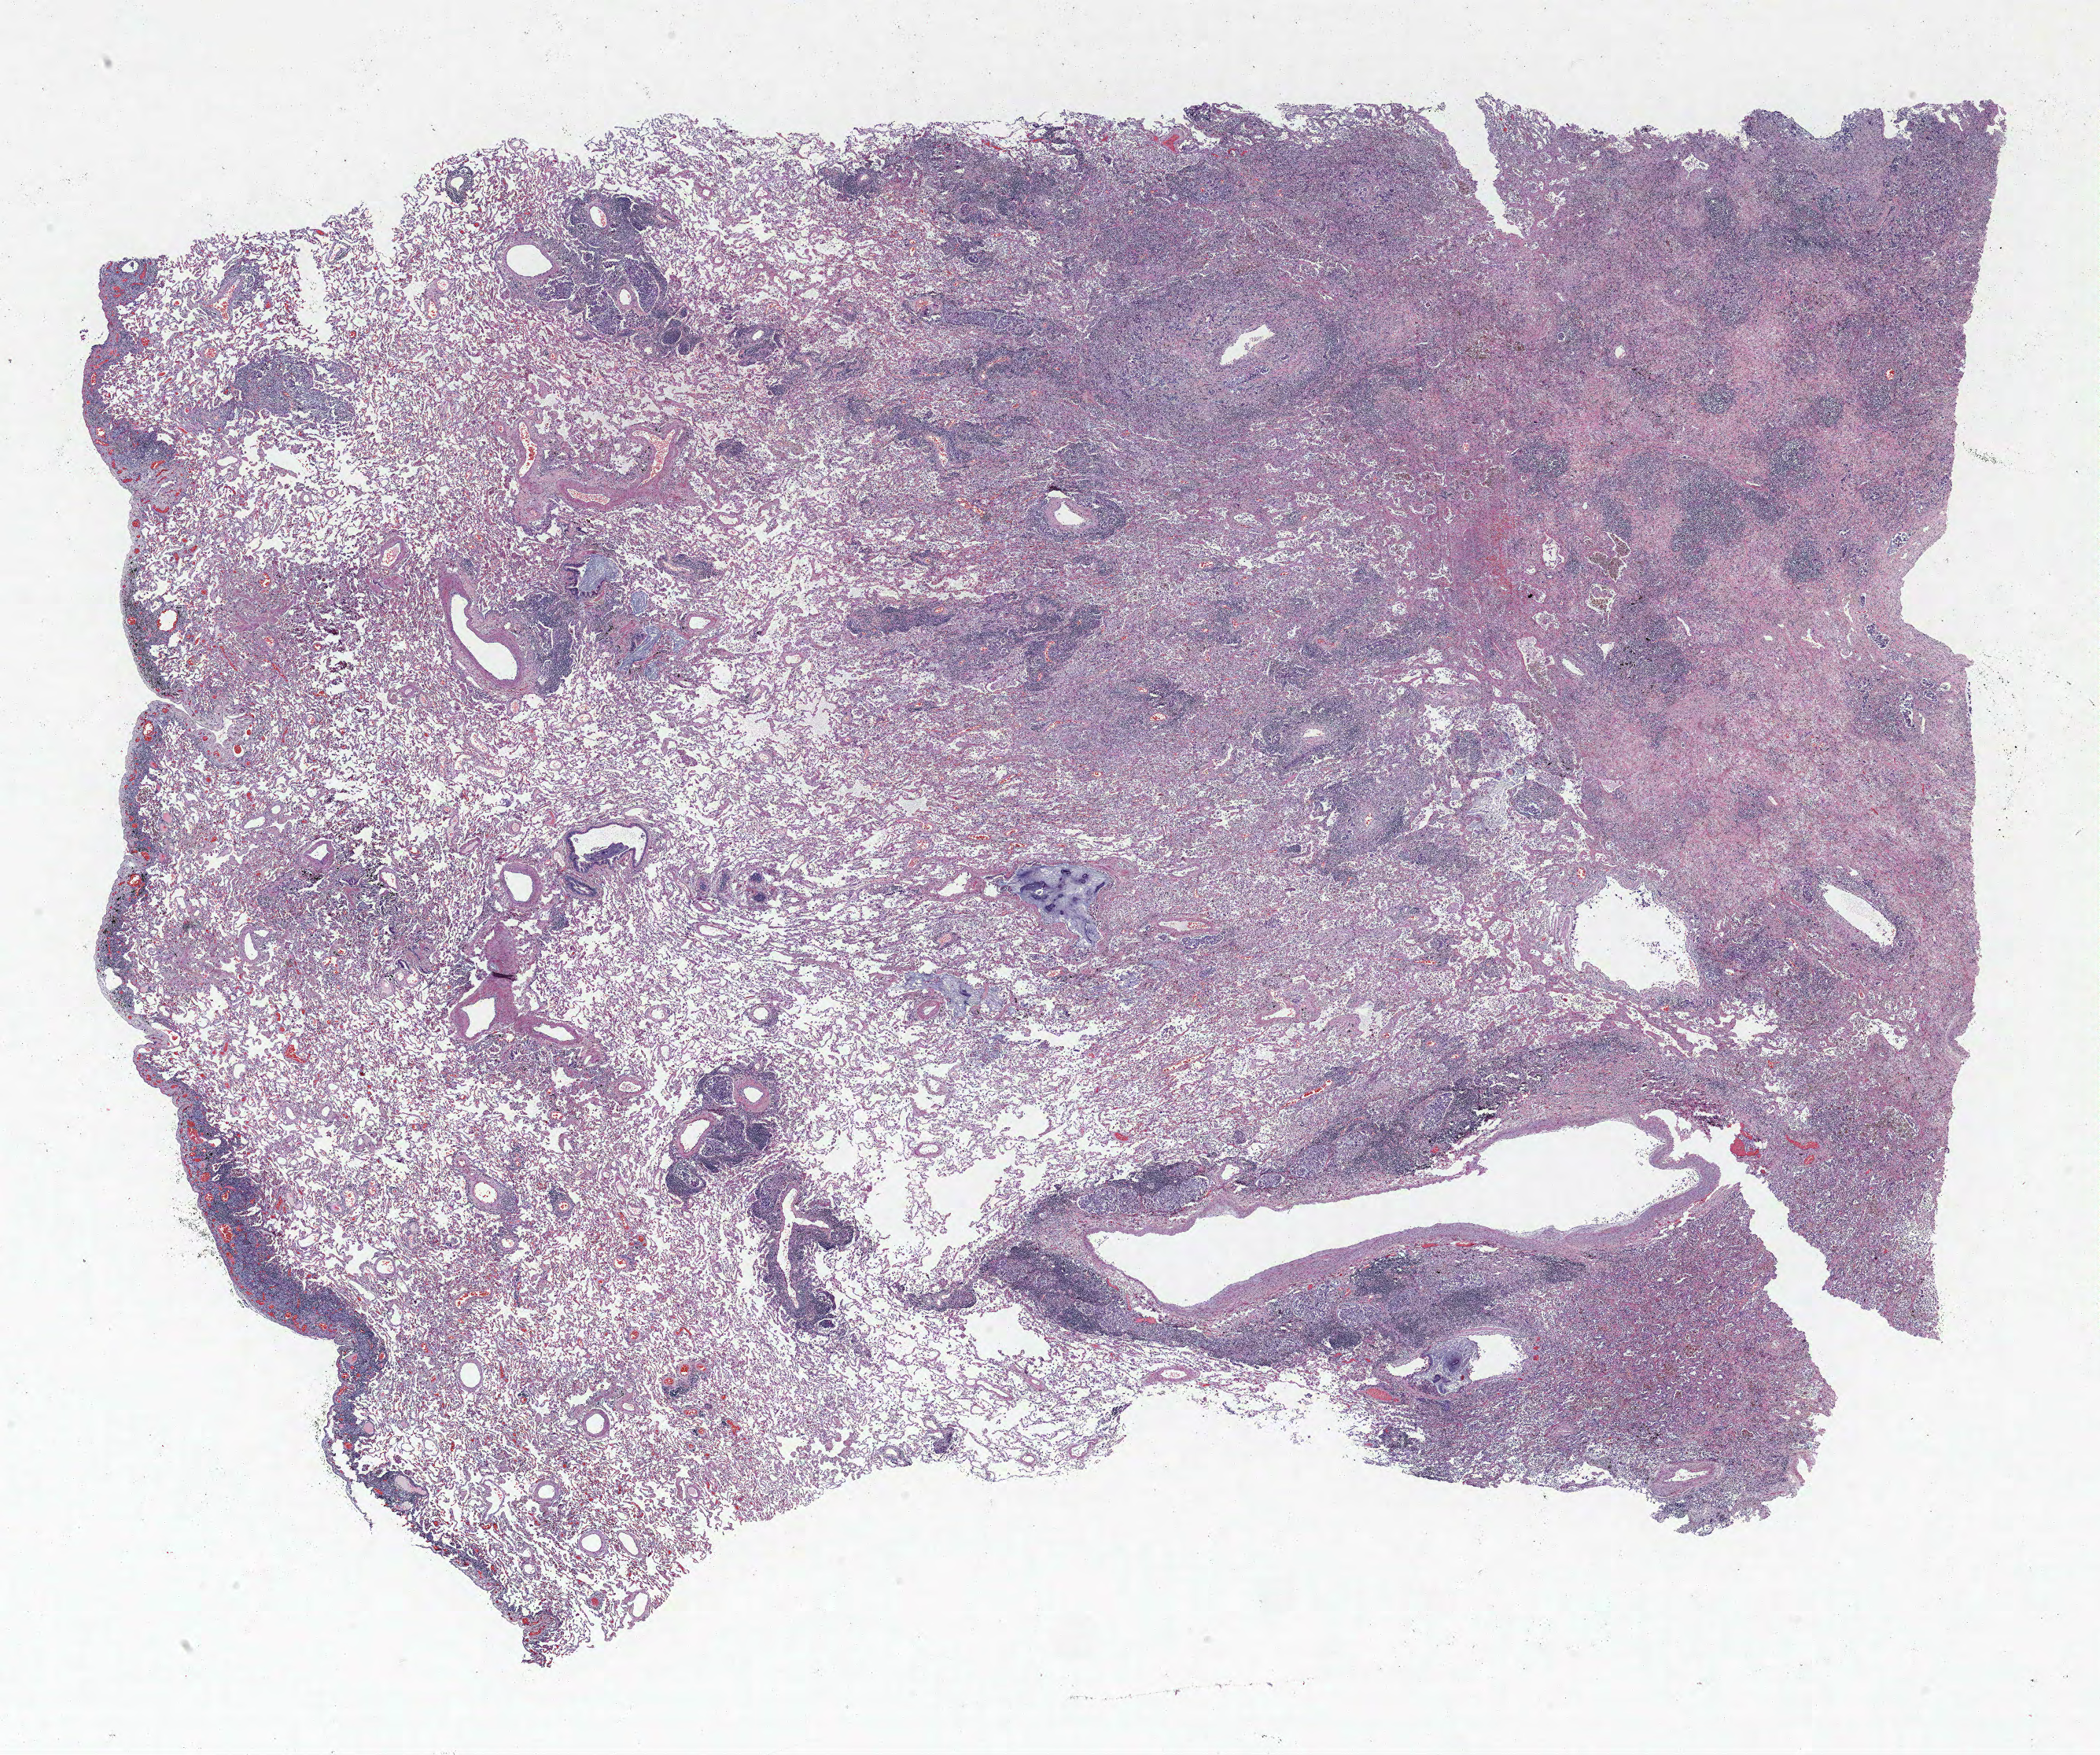
Whole-slide histology image, H&E-stained — low-resolution overview of the scanned area, about 21.4 x 17.9 mm, formalin-fixed paraffin-embedded (FFPE) section, lung. Male patient, aged 65 at enrolment. Current smoker at enrolment. Grade: poorly differentiated (G3).
- participant's lung-cancer diagnosis: Carcinoma, NOS
- stage (AJCC 6th edition): IIIA
- primary tumour location (clinical record): left upper lobe
- tumour size (pathology): 25 mm
- ICD-O-3 topography: upper lobe of lung (C34.1)